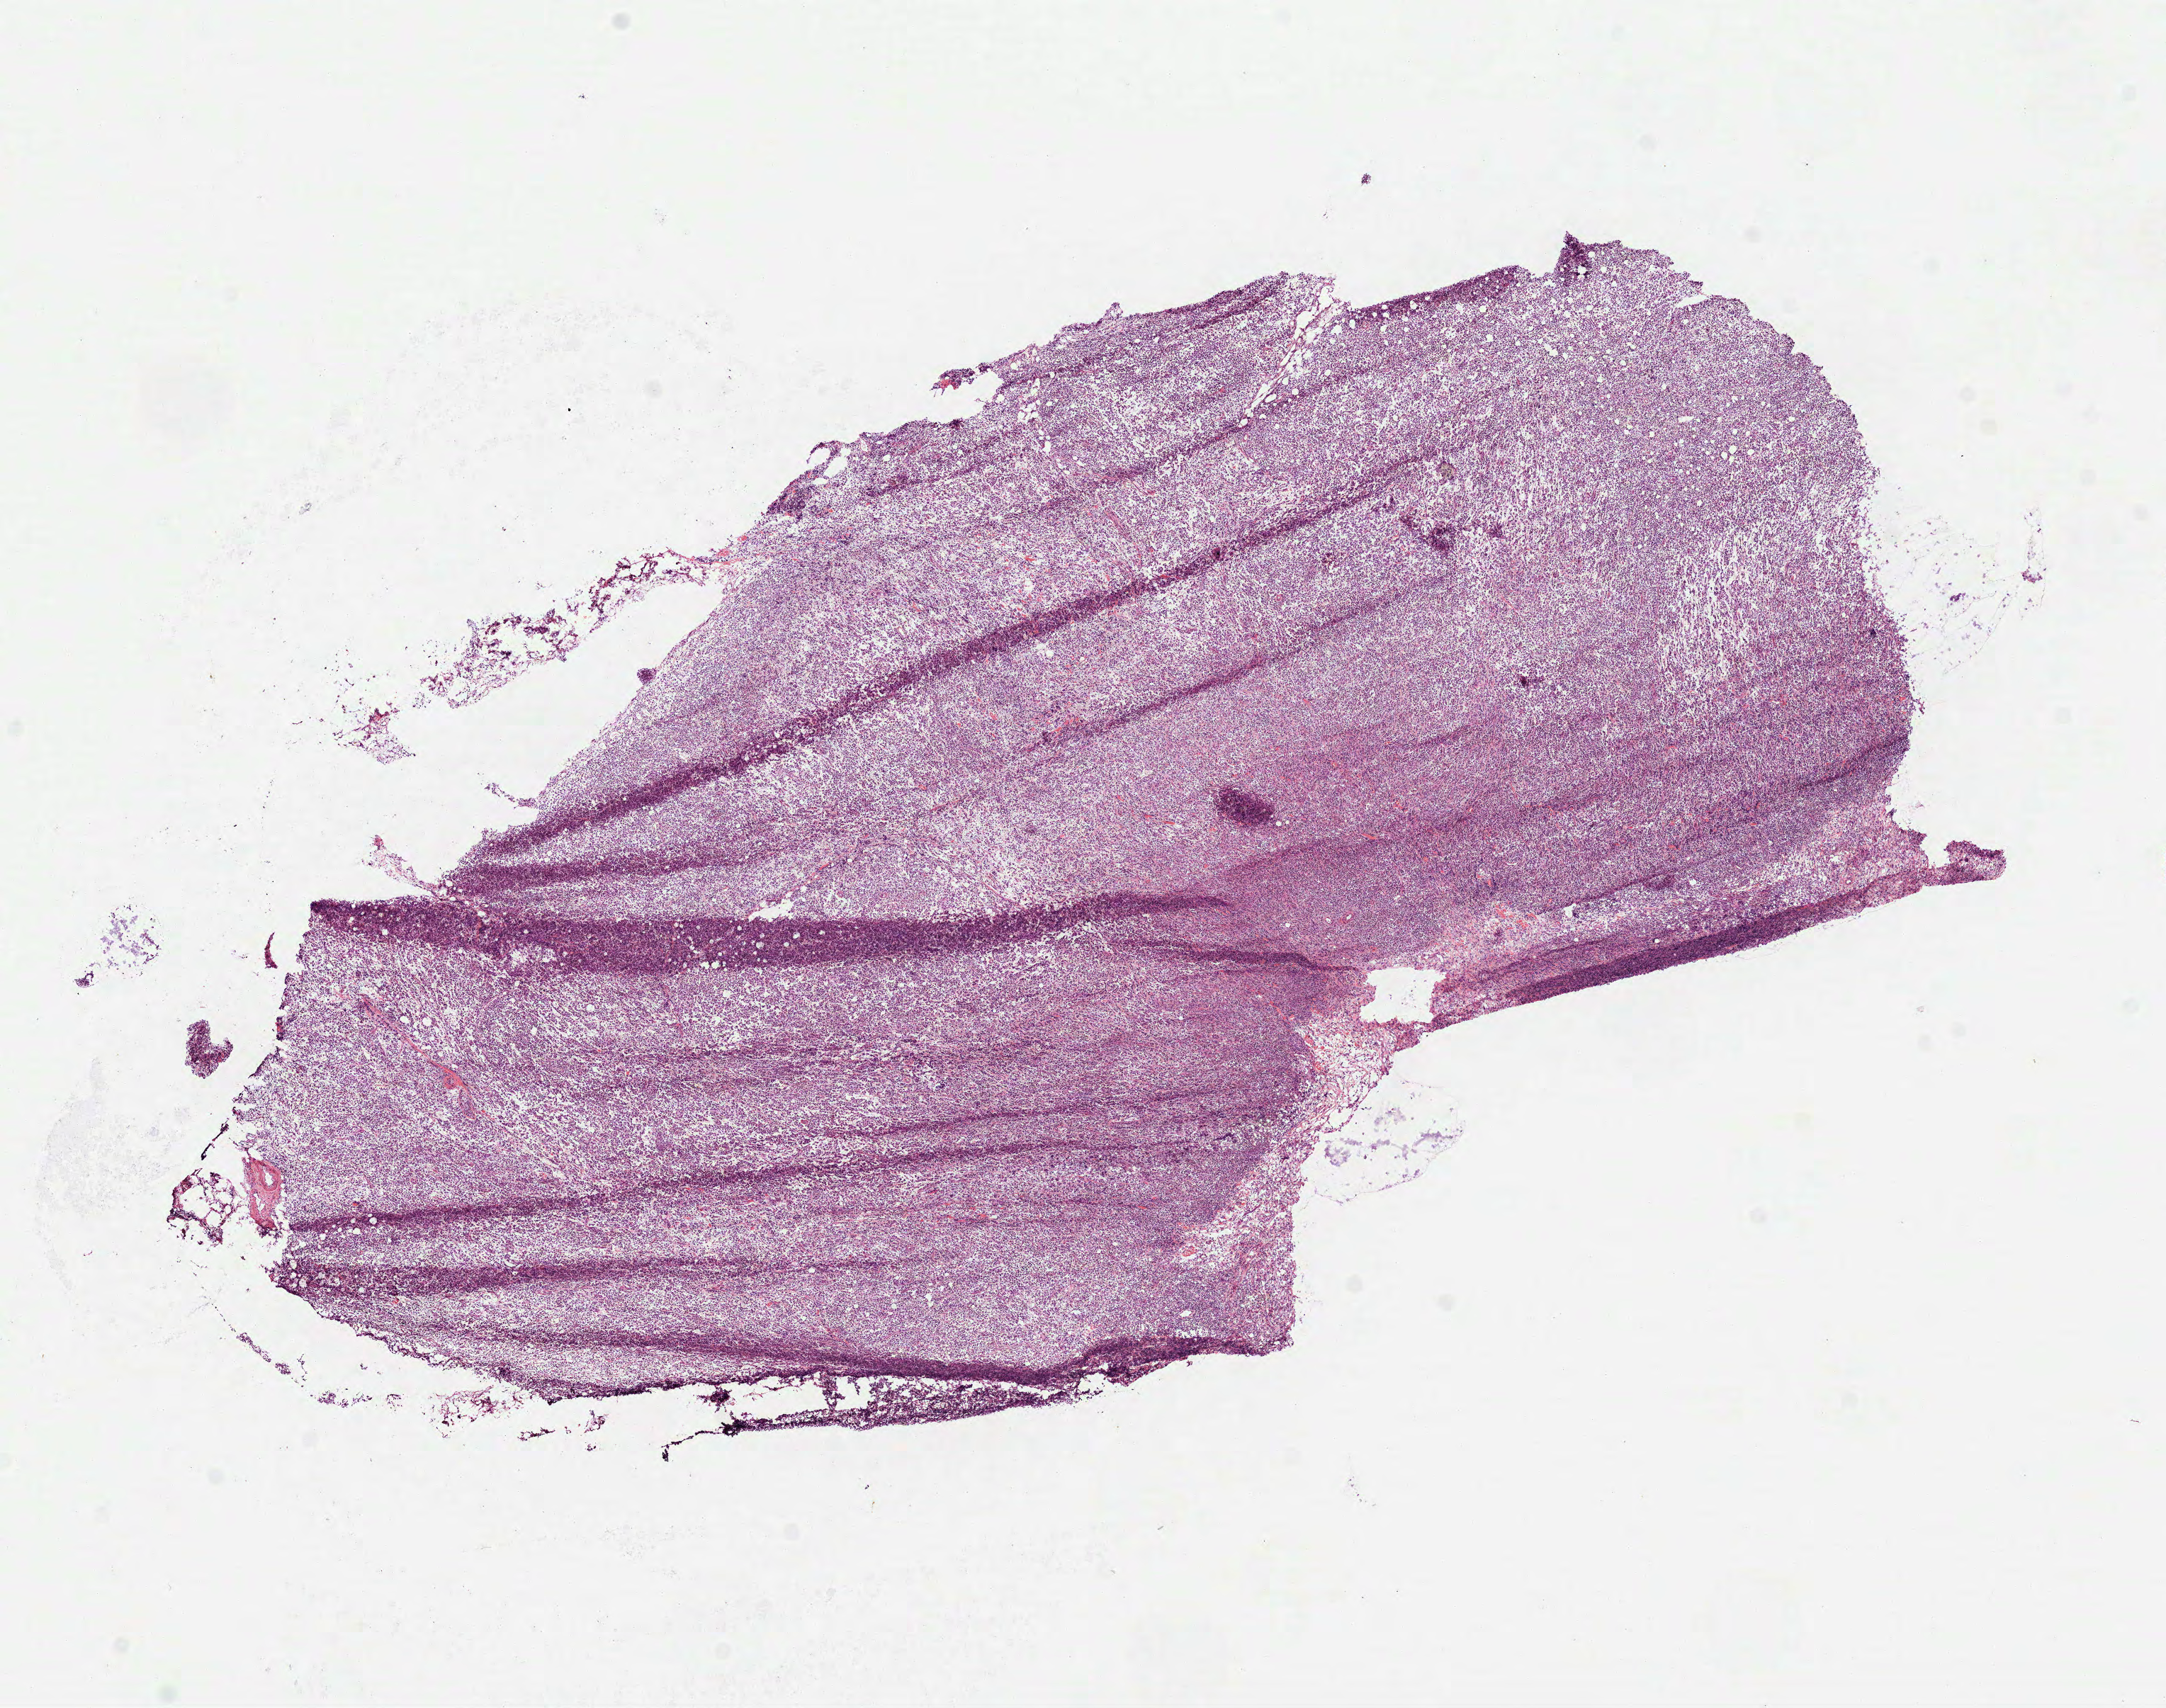
Whole-slide histology image, Hematoxylin and eosin (H&E) stained — low-resolution overview of the scanned area, about 12.3 x 9.7 mm (slide scanned at 40x); frozen section from the top of the tissue portion; lymphoid tissue, primary tumour sample. Male, age 67 years at initial diagnosis. Pathologist review of this section (percent, as recorded): tumour cells 100%, tumour nuclei 95%, normal cells 0%, stromal cells 0%, necrosis 0%. Inflammatory infiltration, as recorded: lymphocyte infiltration 95%, monocyte infiltration 0%, neutrophil infiltration 0%.
Histologic diagnosis: Diffuse large B-cell lymphoma, NOS.